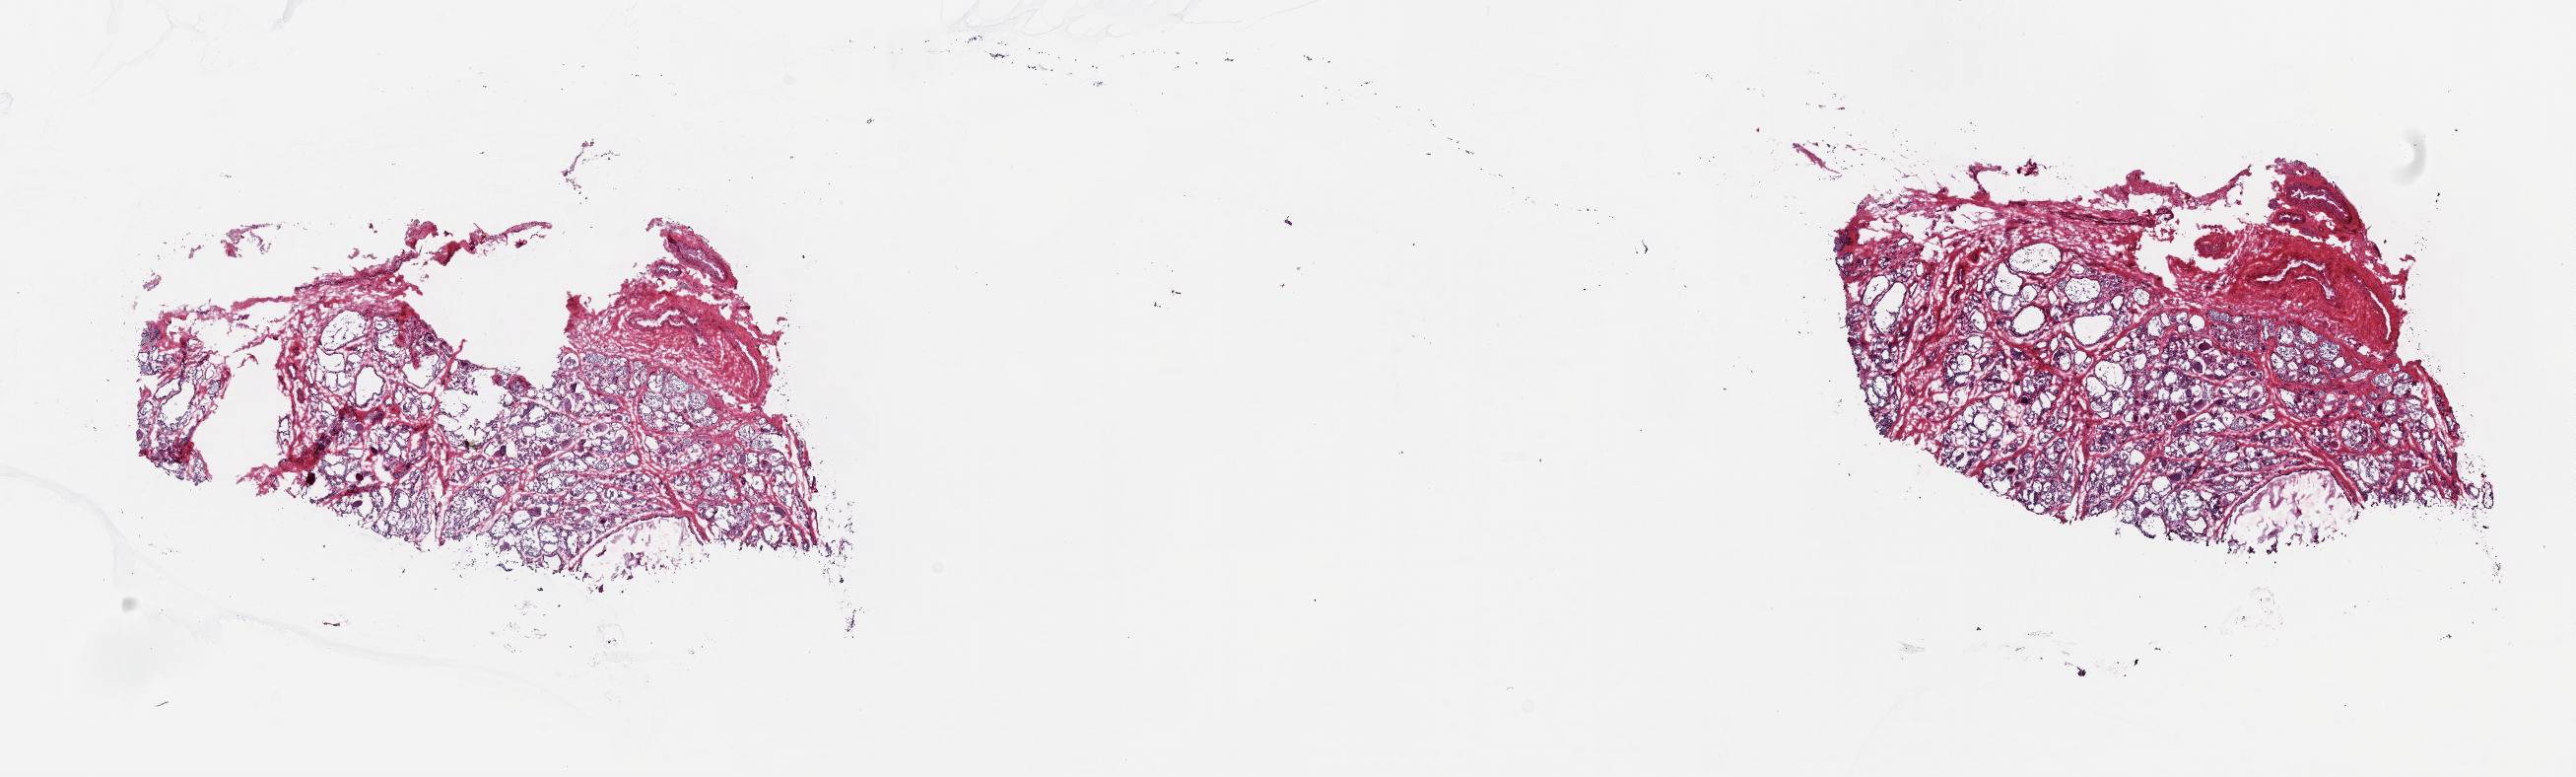
H&E whole-slide image — whole scanned area (about 20.7 x 6.2 mm, slide scanned at 20x) shown as a low-resolution overview. Frozen section from the top of the tissue portion. Solid tissue normal (non-tumour tissue) sample from the thyroid. Male patient; age at initial diagnosis 81 years. Composition of this section per pathologist review: tumour cells 0%, tumour nuclei 0%.
This section: solid tissue normal (non-tumour) sample from the same patient. Patient diagnosis: Papillary adenocarcinoma, NOS (thyroid gland).